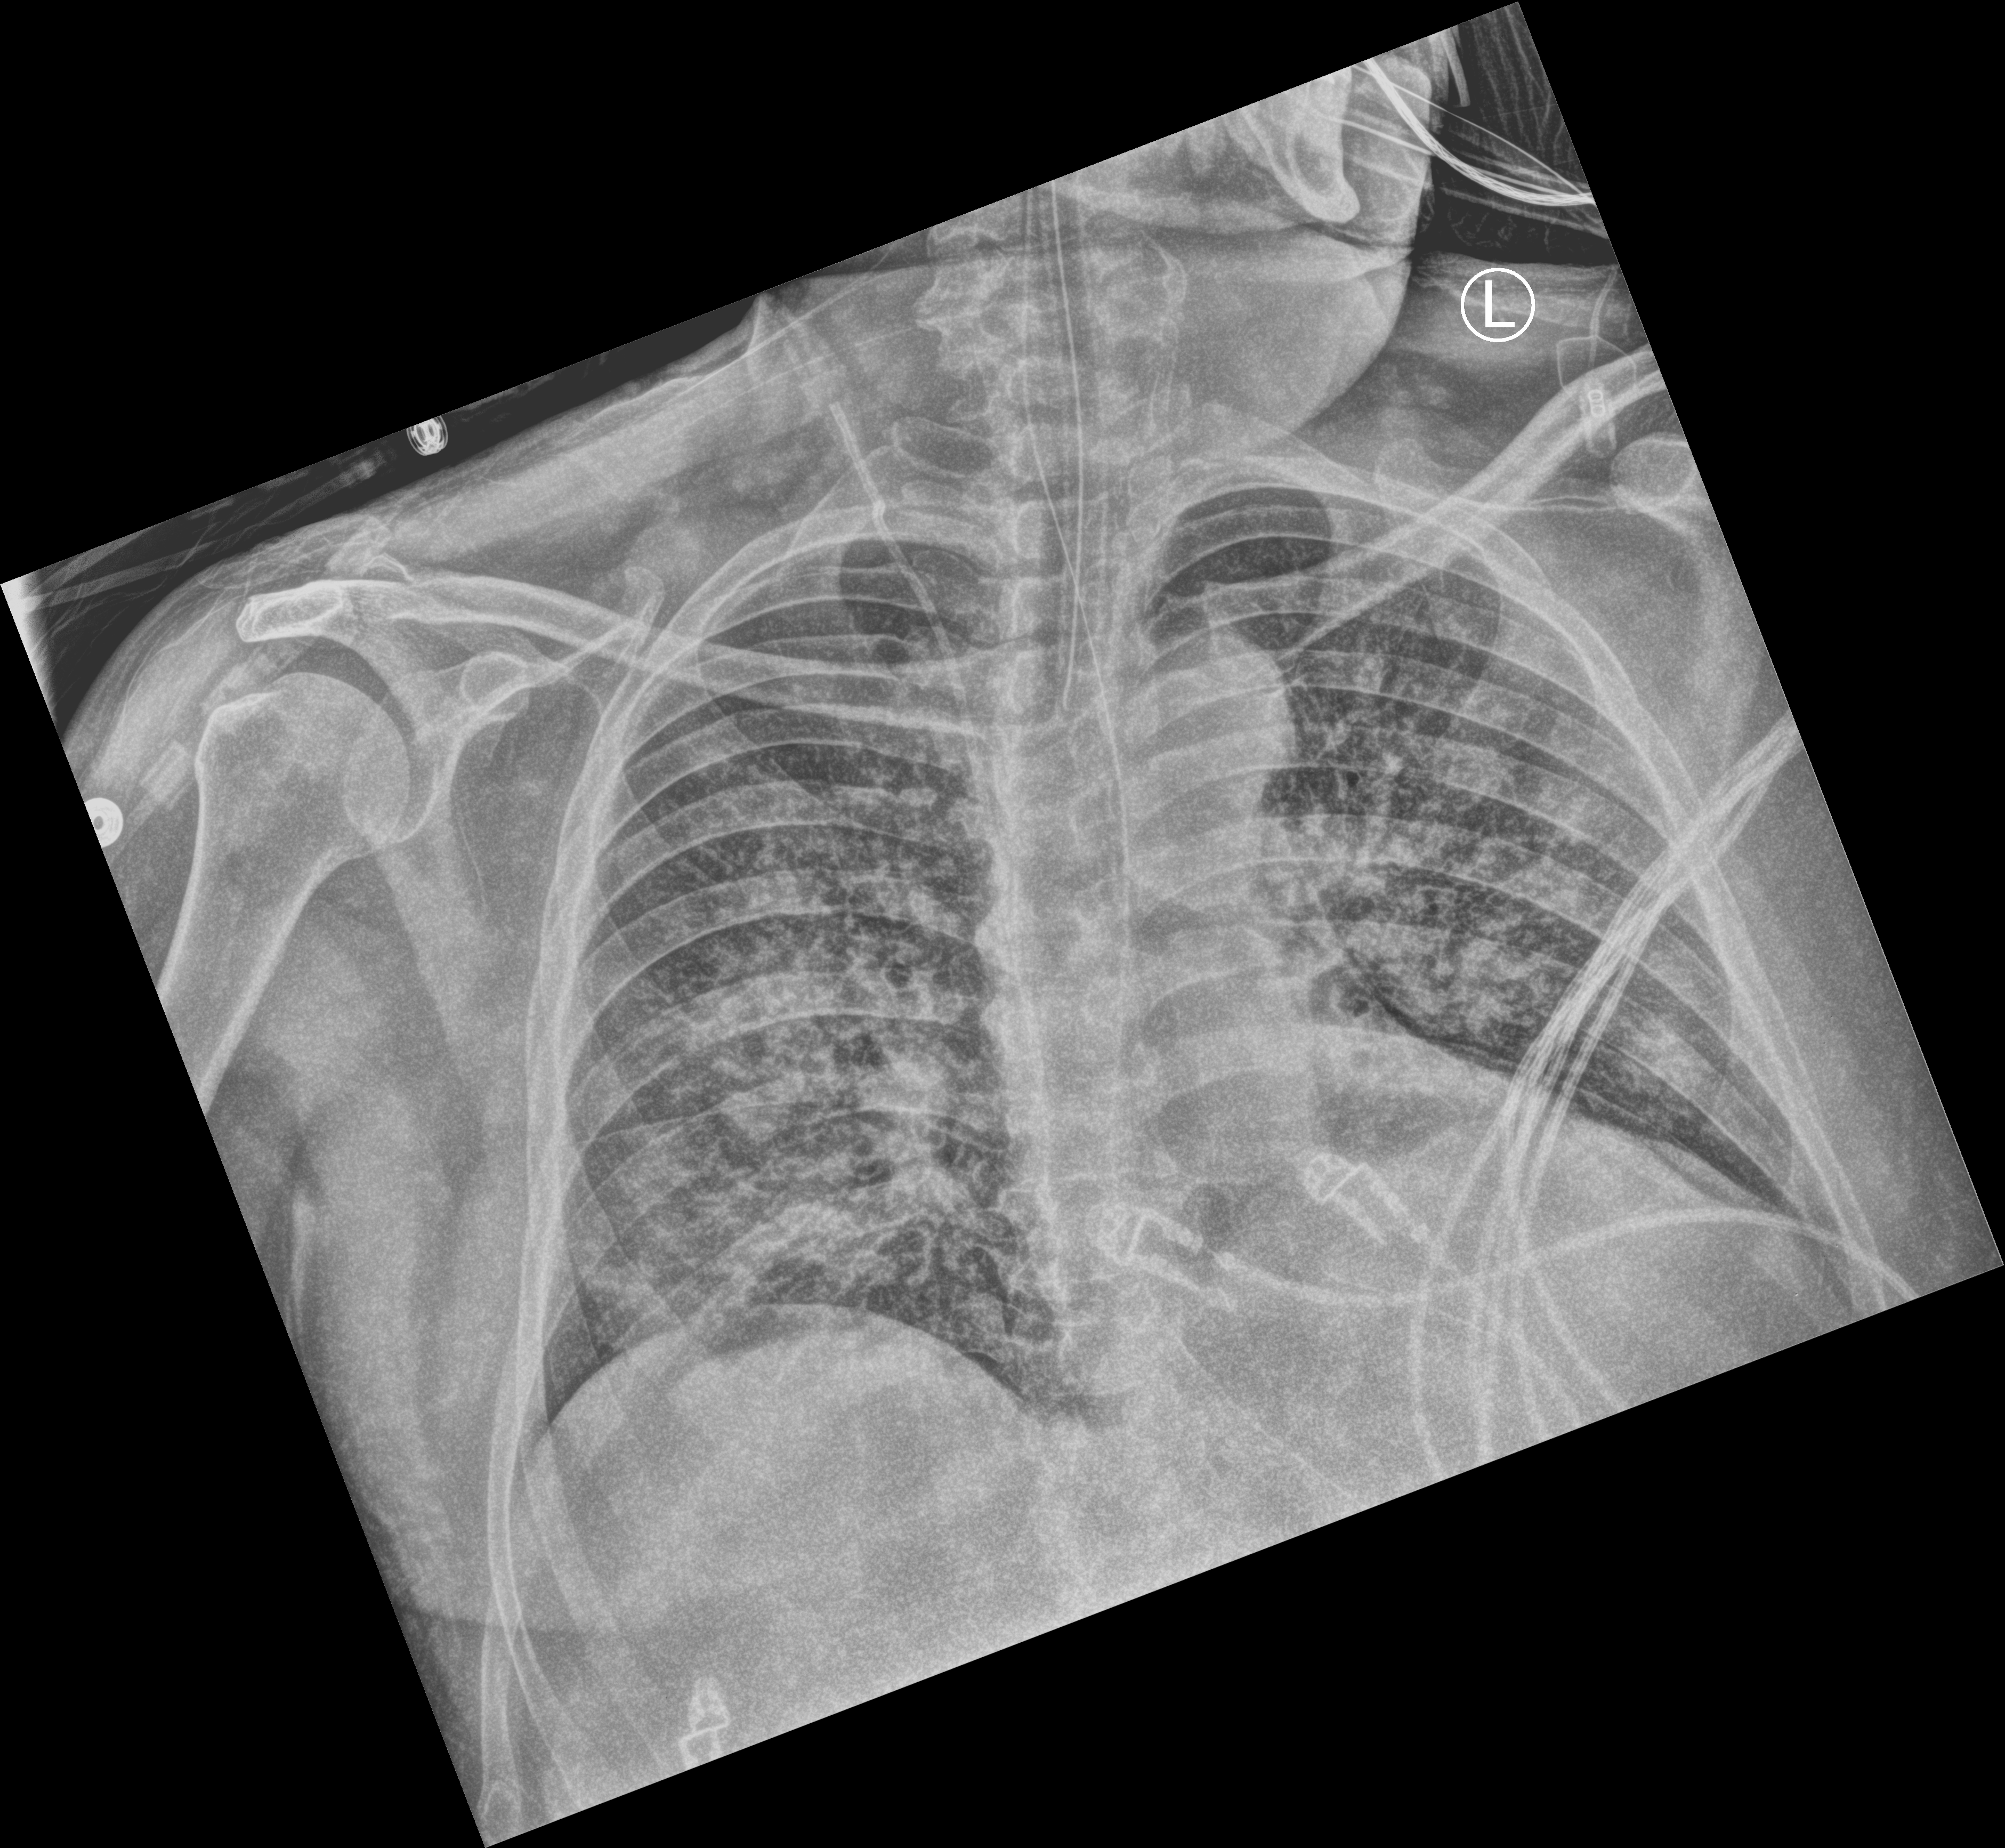
Portable chest radiograph; anteroposterior (AP) projection. Male patient hospitalised with COVID-19, age 60–74 years.
Hospital-stay facts (about this admission, not read from this image; timing relative to this image not recorded): mechanically ventilated during this hospital stay: yes.